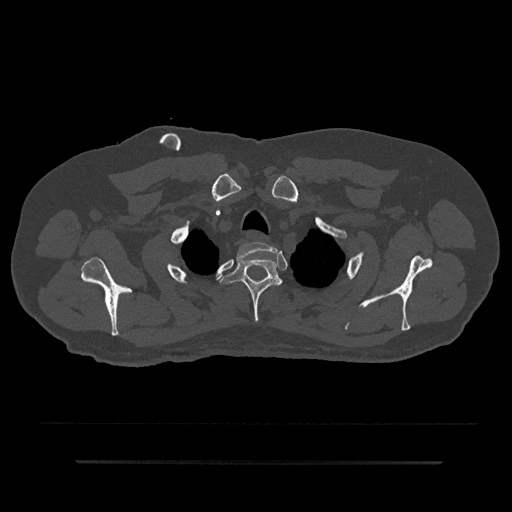
CT including the spine, one axial slice. Position 703 of 797 along the scan axis. Reconstruction kernel Br40s/3. 120 kVp. Bone window (W 1800 / L 400 HU). 0.5 mm slice thickness. 512 × 512 image matrix. Male patient, age 59 years. From the clinical record (not read from this slice): primary cancer: bile ducts; vertebrae with lytic lesions (as recorded): T10.
Annotated regions visible in this slice (semi-automatic segmentation, software-assisted and operator-edited):
- T1 vertebra: box from (x=237, y=242) to (x=276, y=261) px
- T2 vertebra: (x=219, y=255)–(x=282, y=323)